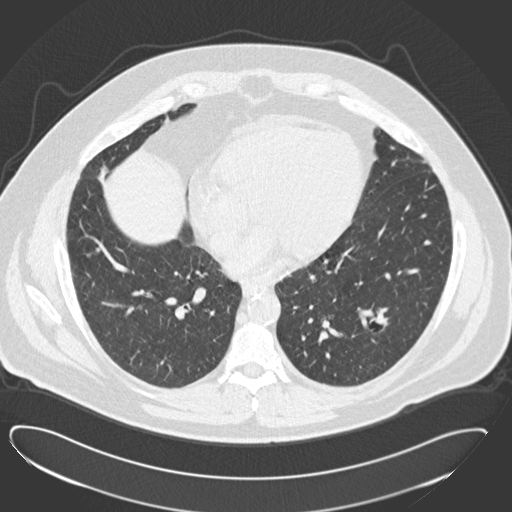
Chest CT (low-dose screening protocol), one axial image, baseline annual screen, lung window (W 1500 / L -600 HU), slice 89 of 183 in the series. Male participant, aged 57 years at enrolment. Current smoker at enrolment.
Expert reader's lesion annotation, bounding box [x1, y1, x2, y2] px = [354, 298, 407, 348]. The screening reader recorded 2 non-calcified nodules or masses ≥4 mm on this exam (left lower lobe, left lower lobe); which of them this box marks is not recorded. Official screen result: positive, change unspecified: nodule(s) >= 4 mm or enlarging nodule(s), mass(es), or other non-specific abnormalities suspicious for lung cancer. Participant outcome: lung cancer diagnosed 791 days after this screen (after the third annual screen) — squamous cell carcinoma, NOS, left lower lobe, moderately differentiated (G2), stage IA (AJCC 6th edition), 22 mm at pathology.